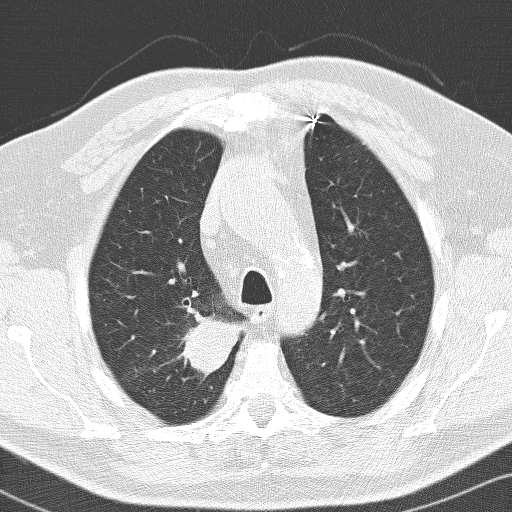
Low-dose screening chest CT, one axial slice. Lung window (W 1500 / L -600 HU). 512 × 512 image matrix, field of view 326 × 326 mm.
Outlined on this slice (expert manual segmentation):
- lesion 1 (tumor, upper lobe of right lung): bounding box <180,309,243,375> (left, top, right, bottom; pixels)